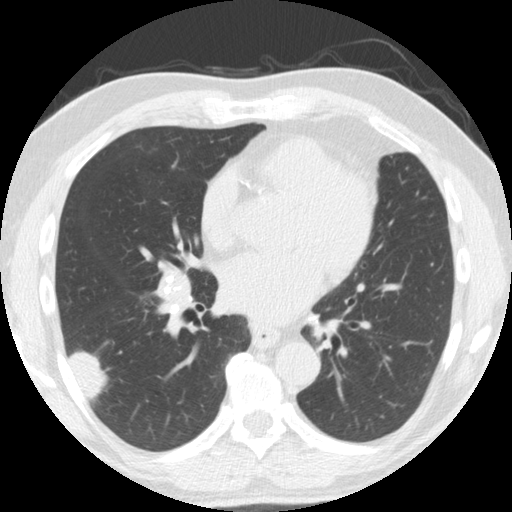
Low-dose screening chest CT, one axial slice; position 80 of 174 along the scan axis; reconstruction kernel STANDARD; lung window (W 1500 / L -600 HU); 2.5 mm slice thickness; 512 × 512 image matrix.
Annotated regions visible in this slice (expert manual segmentation):
- lesion 1 (tumor, lower lobe of right lung): bounding box (x1, y1, x2, y2) in pixels: (69, 351, 107, 399)